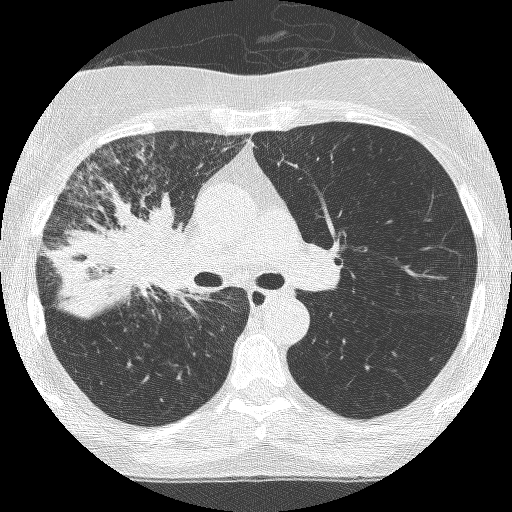
Chest CT (low-dose screening protocol), one axial image, third screening round (two years after baseline), lung window (W 1500 / L -600 HU), 1.25 mm slice thickness, 120 kVp, slice 161 of 253 in the series. Female participant, aged 64 years at enrolment.
Expert reader's lesion annotation, box from (x=79, y=201) to (x=204, y=327) px. Reader record for this screening exam (exam-level; its link to the box is not recorded): non-calcified nodule or mass ≥4 mm, right upper lobe, 49 × 43 mm, spiculated (stellate) margins, soft tissue attenuation, pre-existing on the prior screen: yes; interval growth: yes. Official screen result: positive, other. Participant outcome: lung cancer diagnosed 7 days after this screen — adenocarcinoma, NOS, right upper lobe, right middle lobe, right hilum, stage IV (AJCC 6th edition), 85 mm at pathology.